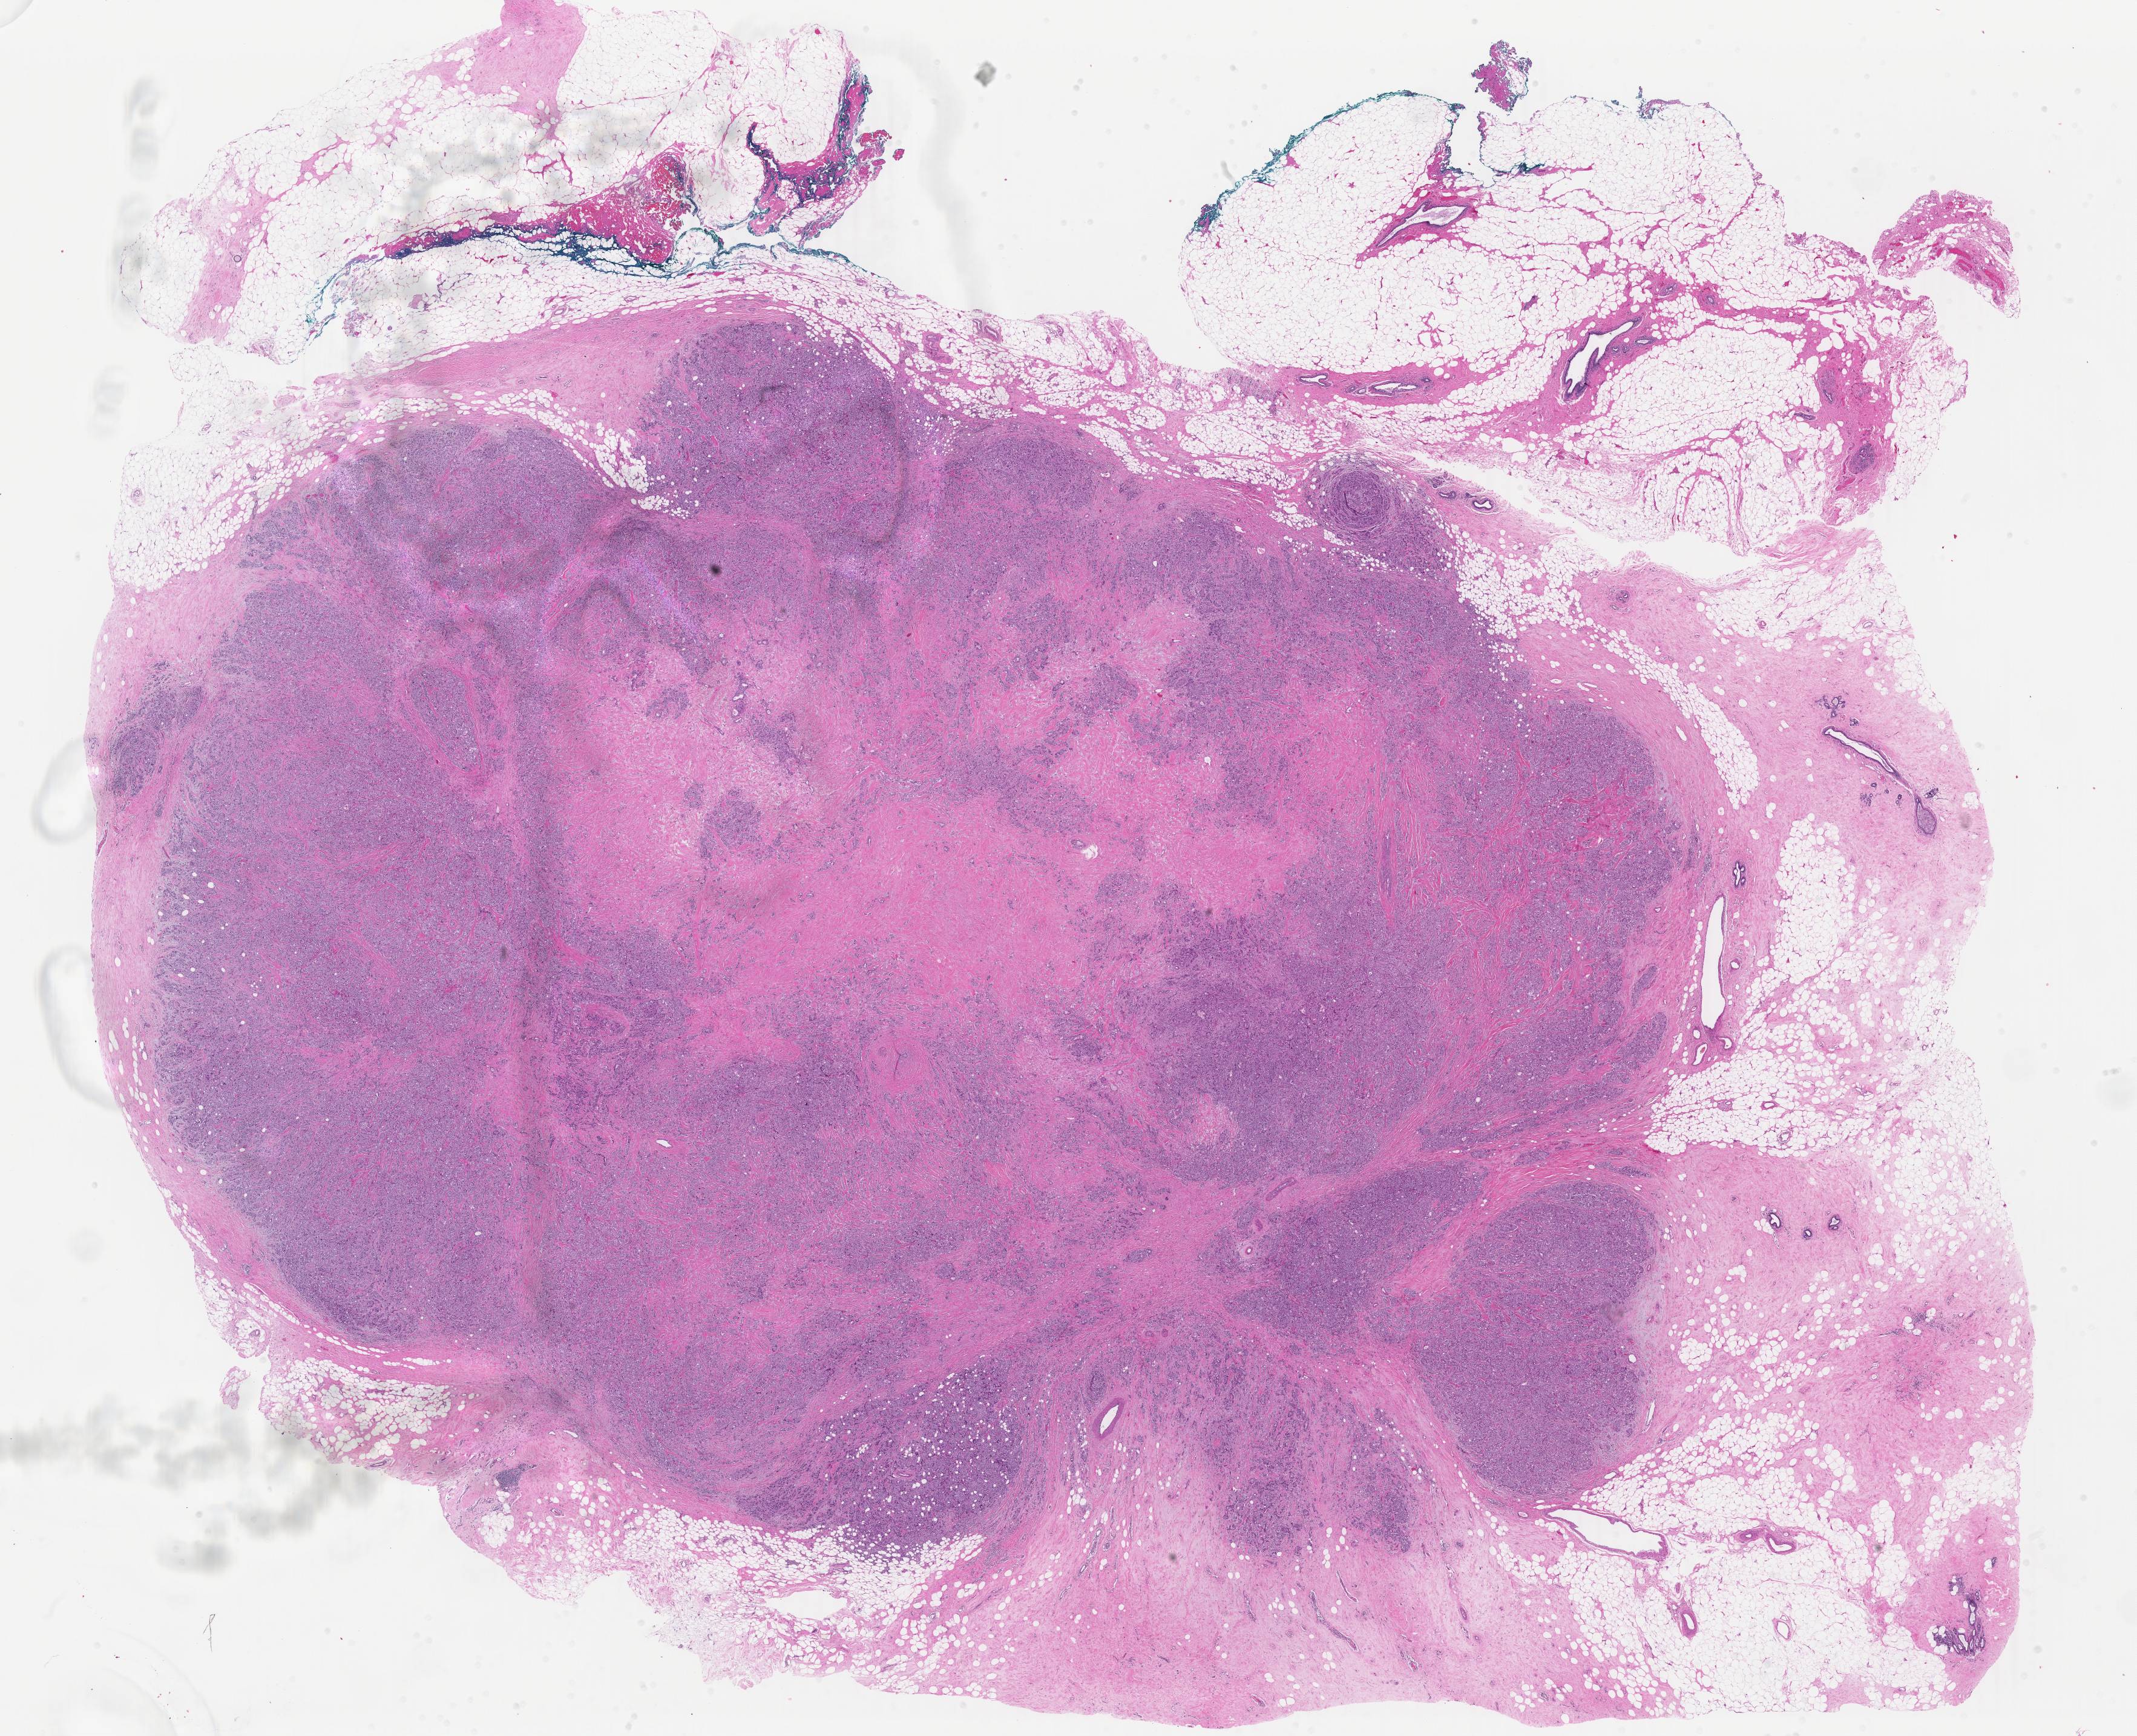
Digitized Hematoxylin and eosin (H&E) stained tissue section (whole slide) — low-resolution overview of the scanned area, about 28.1 x 22.8 mm (from a 40x scan); FFPE section; primary tumour sample from the breast. Female patient; age at initial diagnosis 62 years.
AJCC pathologic stage: IIB. Lymph nodes positive (case pathology): 1 of 23 examined. Pathologic diagnosis: Infiltrating duct carcinoma, NOS. Laterality: right.